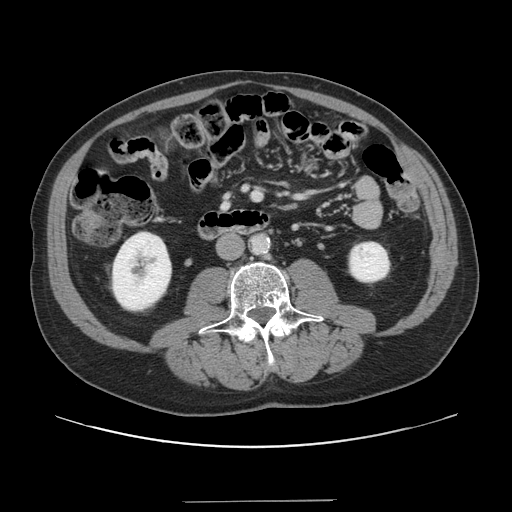
Contrast-enhanced abdominal CT, one axial slice. Slice 30 of 151 in the series (ordered by position). Soft-tissue window (W 400 / L 40 HU). 512 × 512 image matrix. Male patient, age 63 years. From the clinical record (not read from this slice): diagnosis: colorectal cancer liver metastases, imaged before liver resection; multiple liver metastases: no; largest metastasis: 2.1 cm.
Annotated regions visible in this slice (manually delineated by an expert):
- portal vein (with intrahepatic branches): bounding box <253,193,259,196> (left, top, right, bottom; pixels)